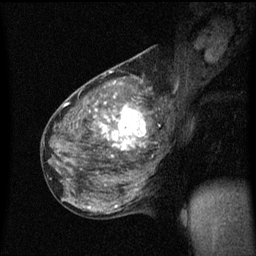
Breast MRI (dynamic contrast-enhanced), one sagittal slice; slice 29 of 60 in the series (ordered by position); dynamic contrast-enhanced series, image 2 of 3 at this slice position (ordered by acquisition); 1.5 T; TE 4.2 ms, TR 8.4 ms; 2 mm slice thickness; 256 × 256 image matrix, field of view 200 × 200 mm. Female patient, age 49 years.
Annotated regions visible in this slice (semi-automatic segmentation, software-assisted and operator-edited):
- analysis volume of interest (the breast-tissue region the enhancement analysis was run in; not a lesion): bounding box [x1, y1, x2, y2] px = [103, 90, 157, 151]
- tumour enhancement mask (voxels above the 70 % enhancement threshold inside the analysis volume of interest): [103, 96, 147, 151]